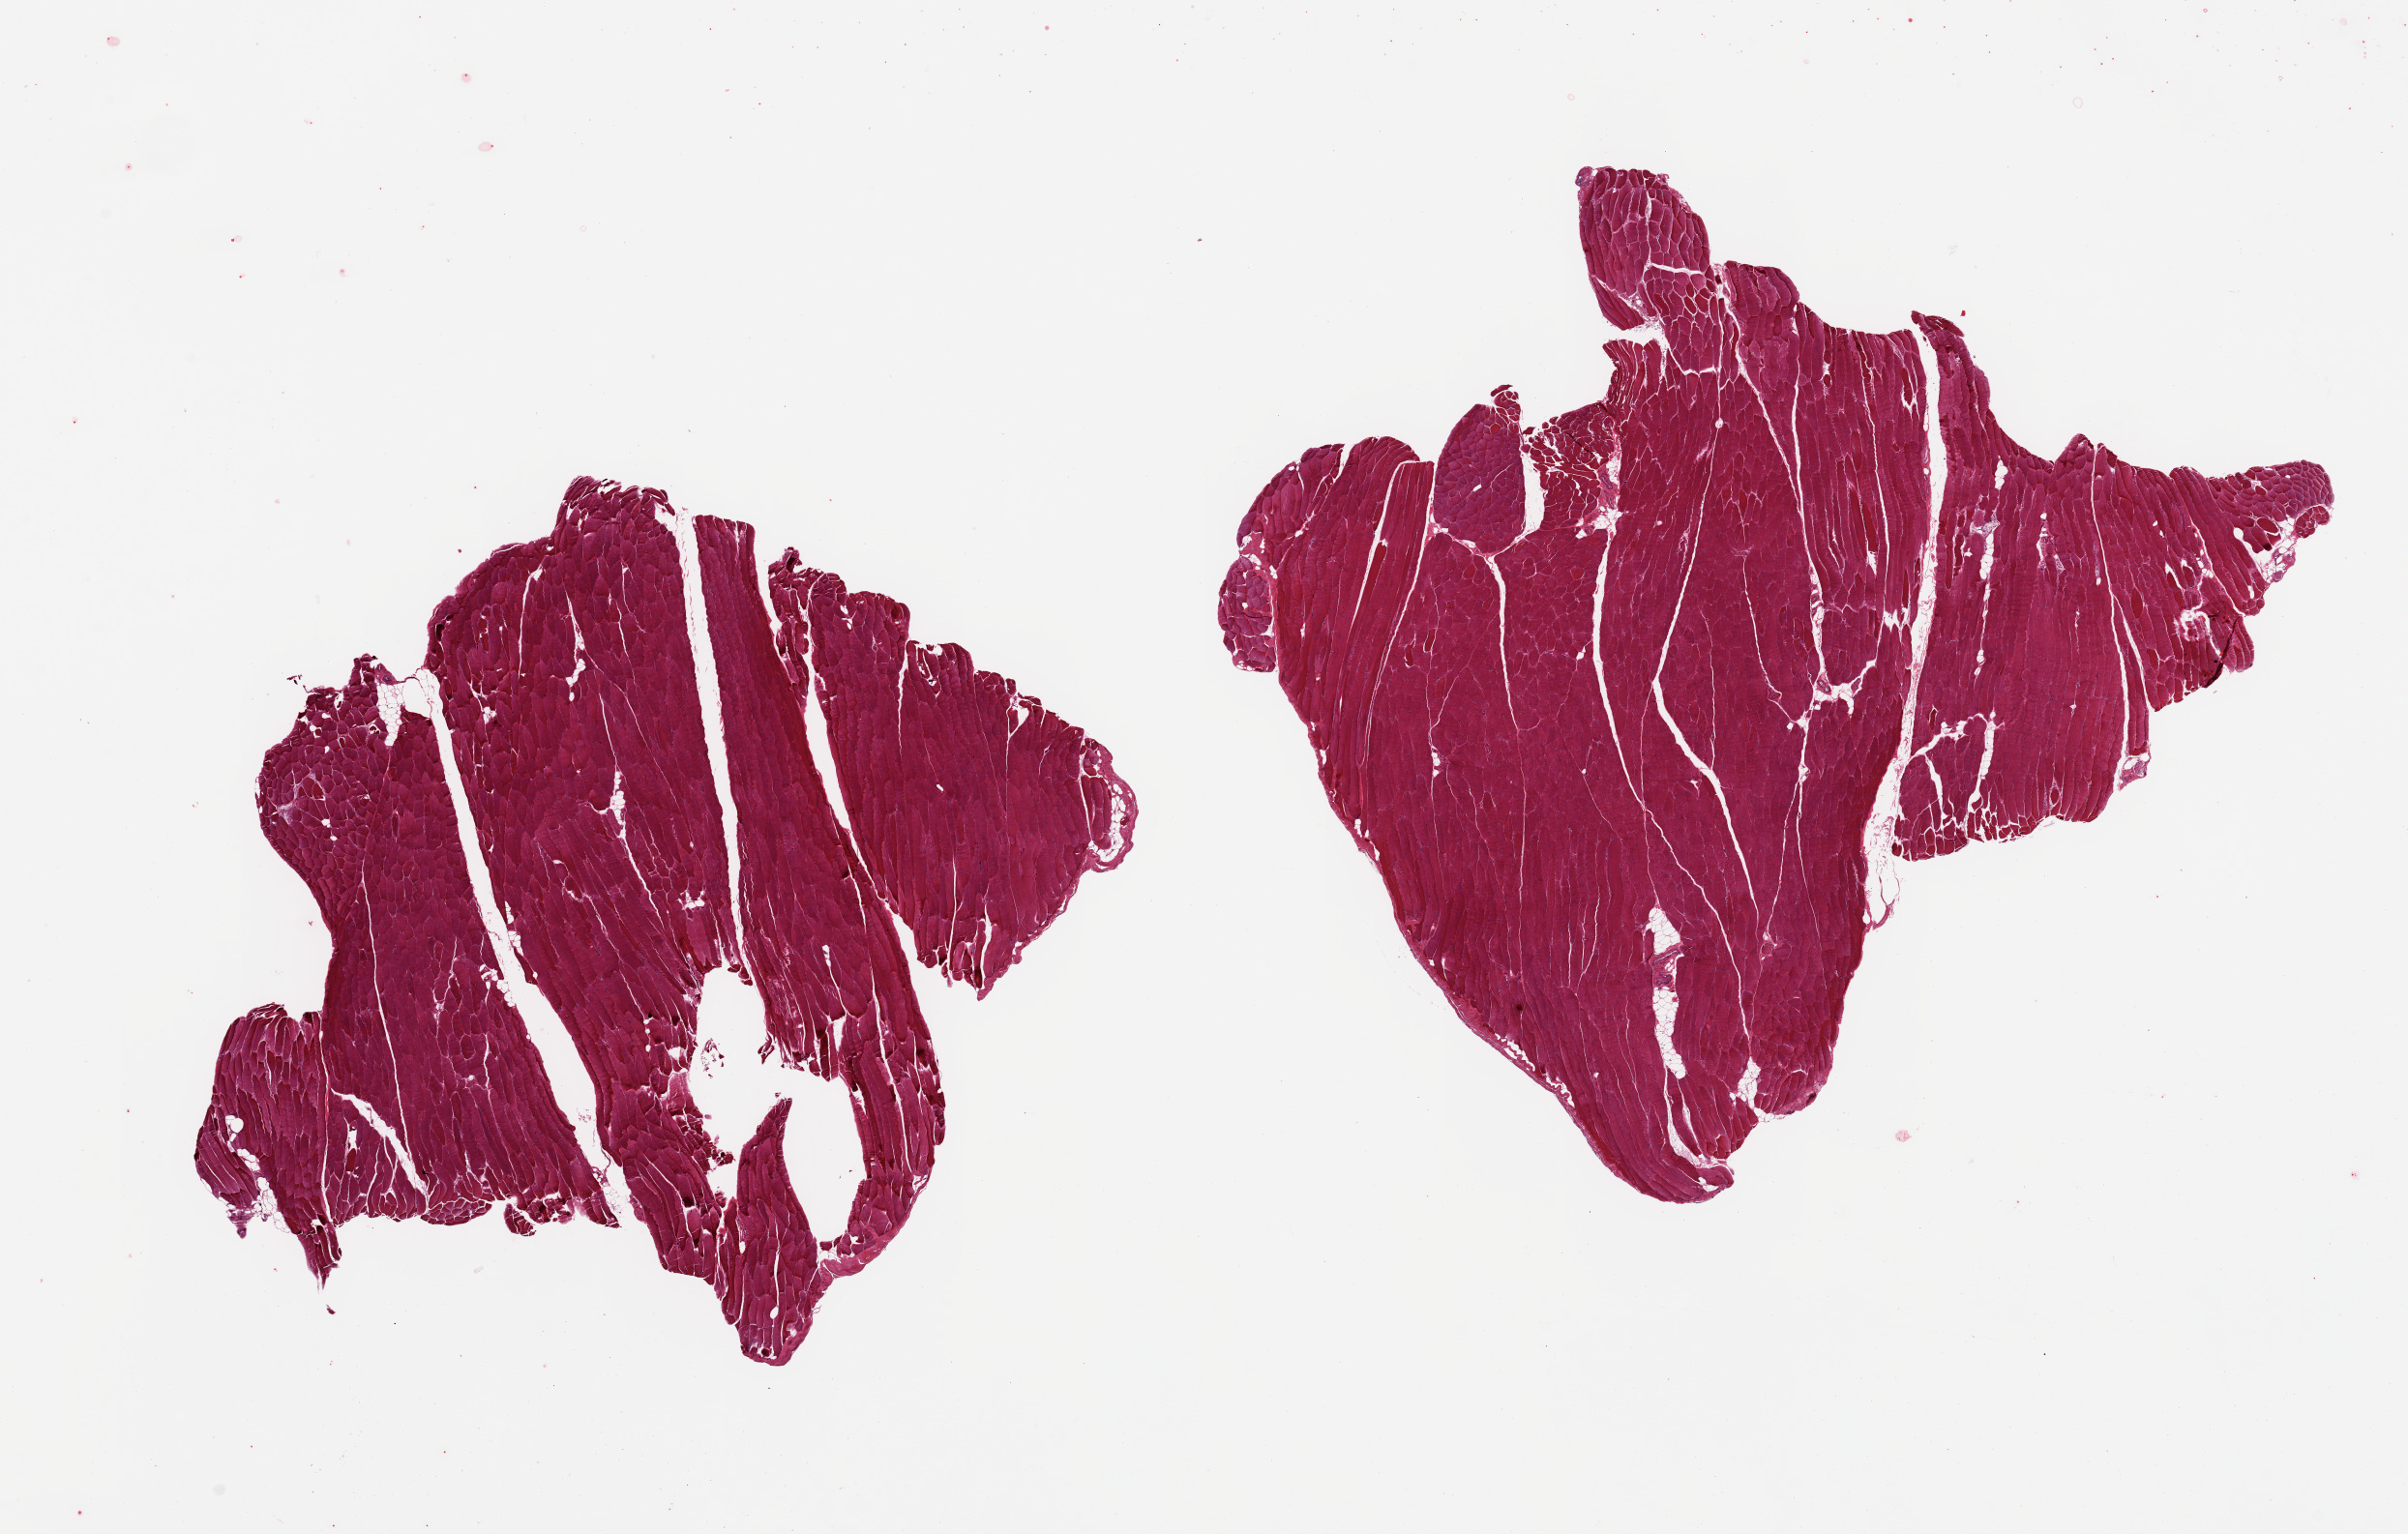
Digitized hematoxylin and eosin (H&E)-stained section — low-resolution overview of the scanned area, about 19.7 x 12.5 mm (acquisition: 20x scan); PAXgene-fixed, paraffin-embedded tissue; target tissue: skeletal muscle; donor tissue sample. Female donor.
Reviewer comment on this tissue sample: 2 pieces; minimal internal fat; no atrophy.